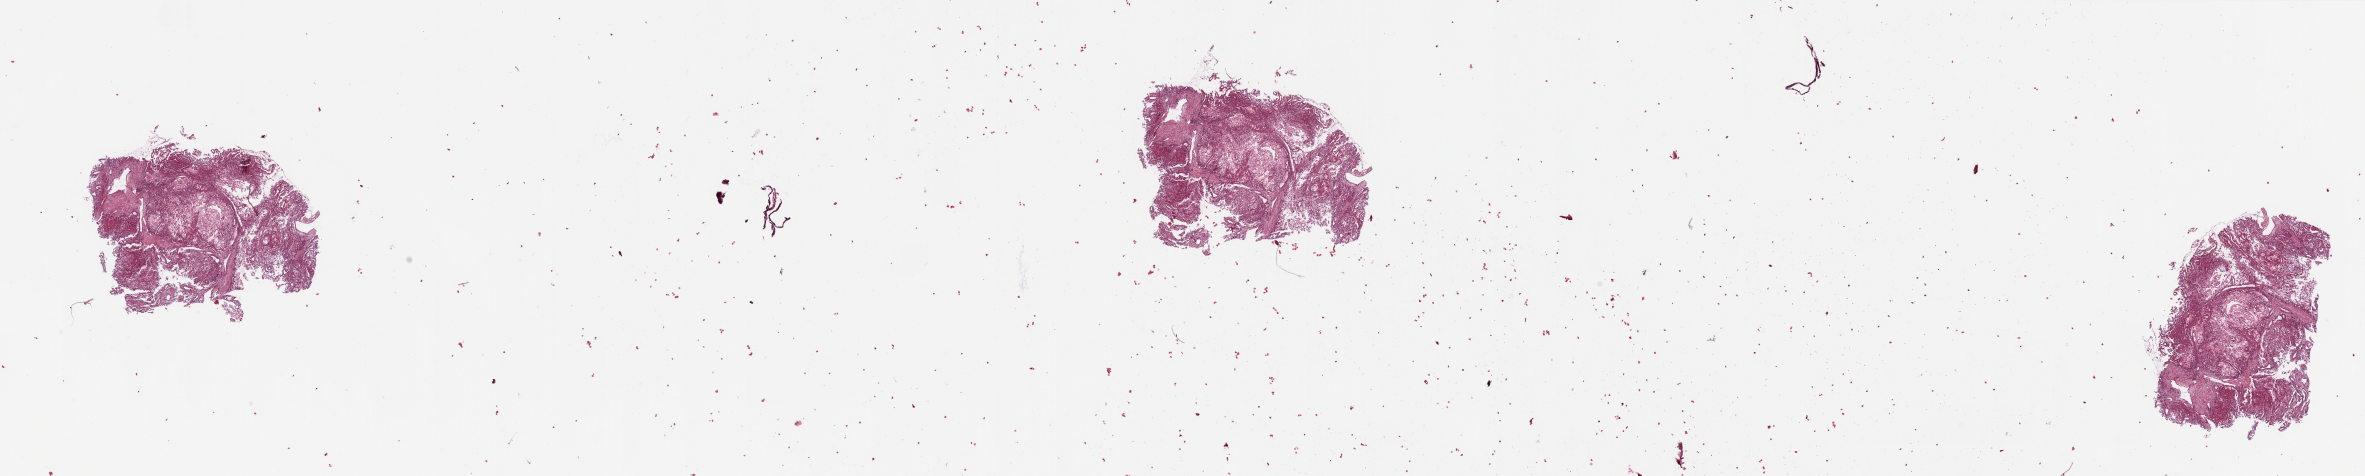
Whole-slide histology image, H&E — whole scanned area (about 37.4 x 7.5 mm, acquisition: 20x scan) shown as a low-resolution overview; tumour tissue sample, sampled site: kidney. 69-year-old male patient. Composition of this section per pathologist review: tumour nuclei 80%, necrosis 2%.
Diagnosis: Renal cell carcinoma, NOS.